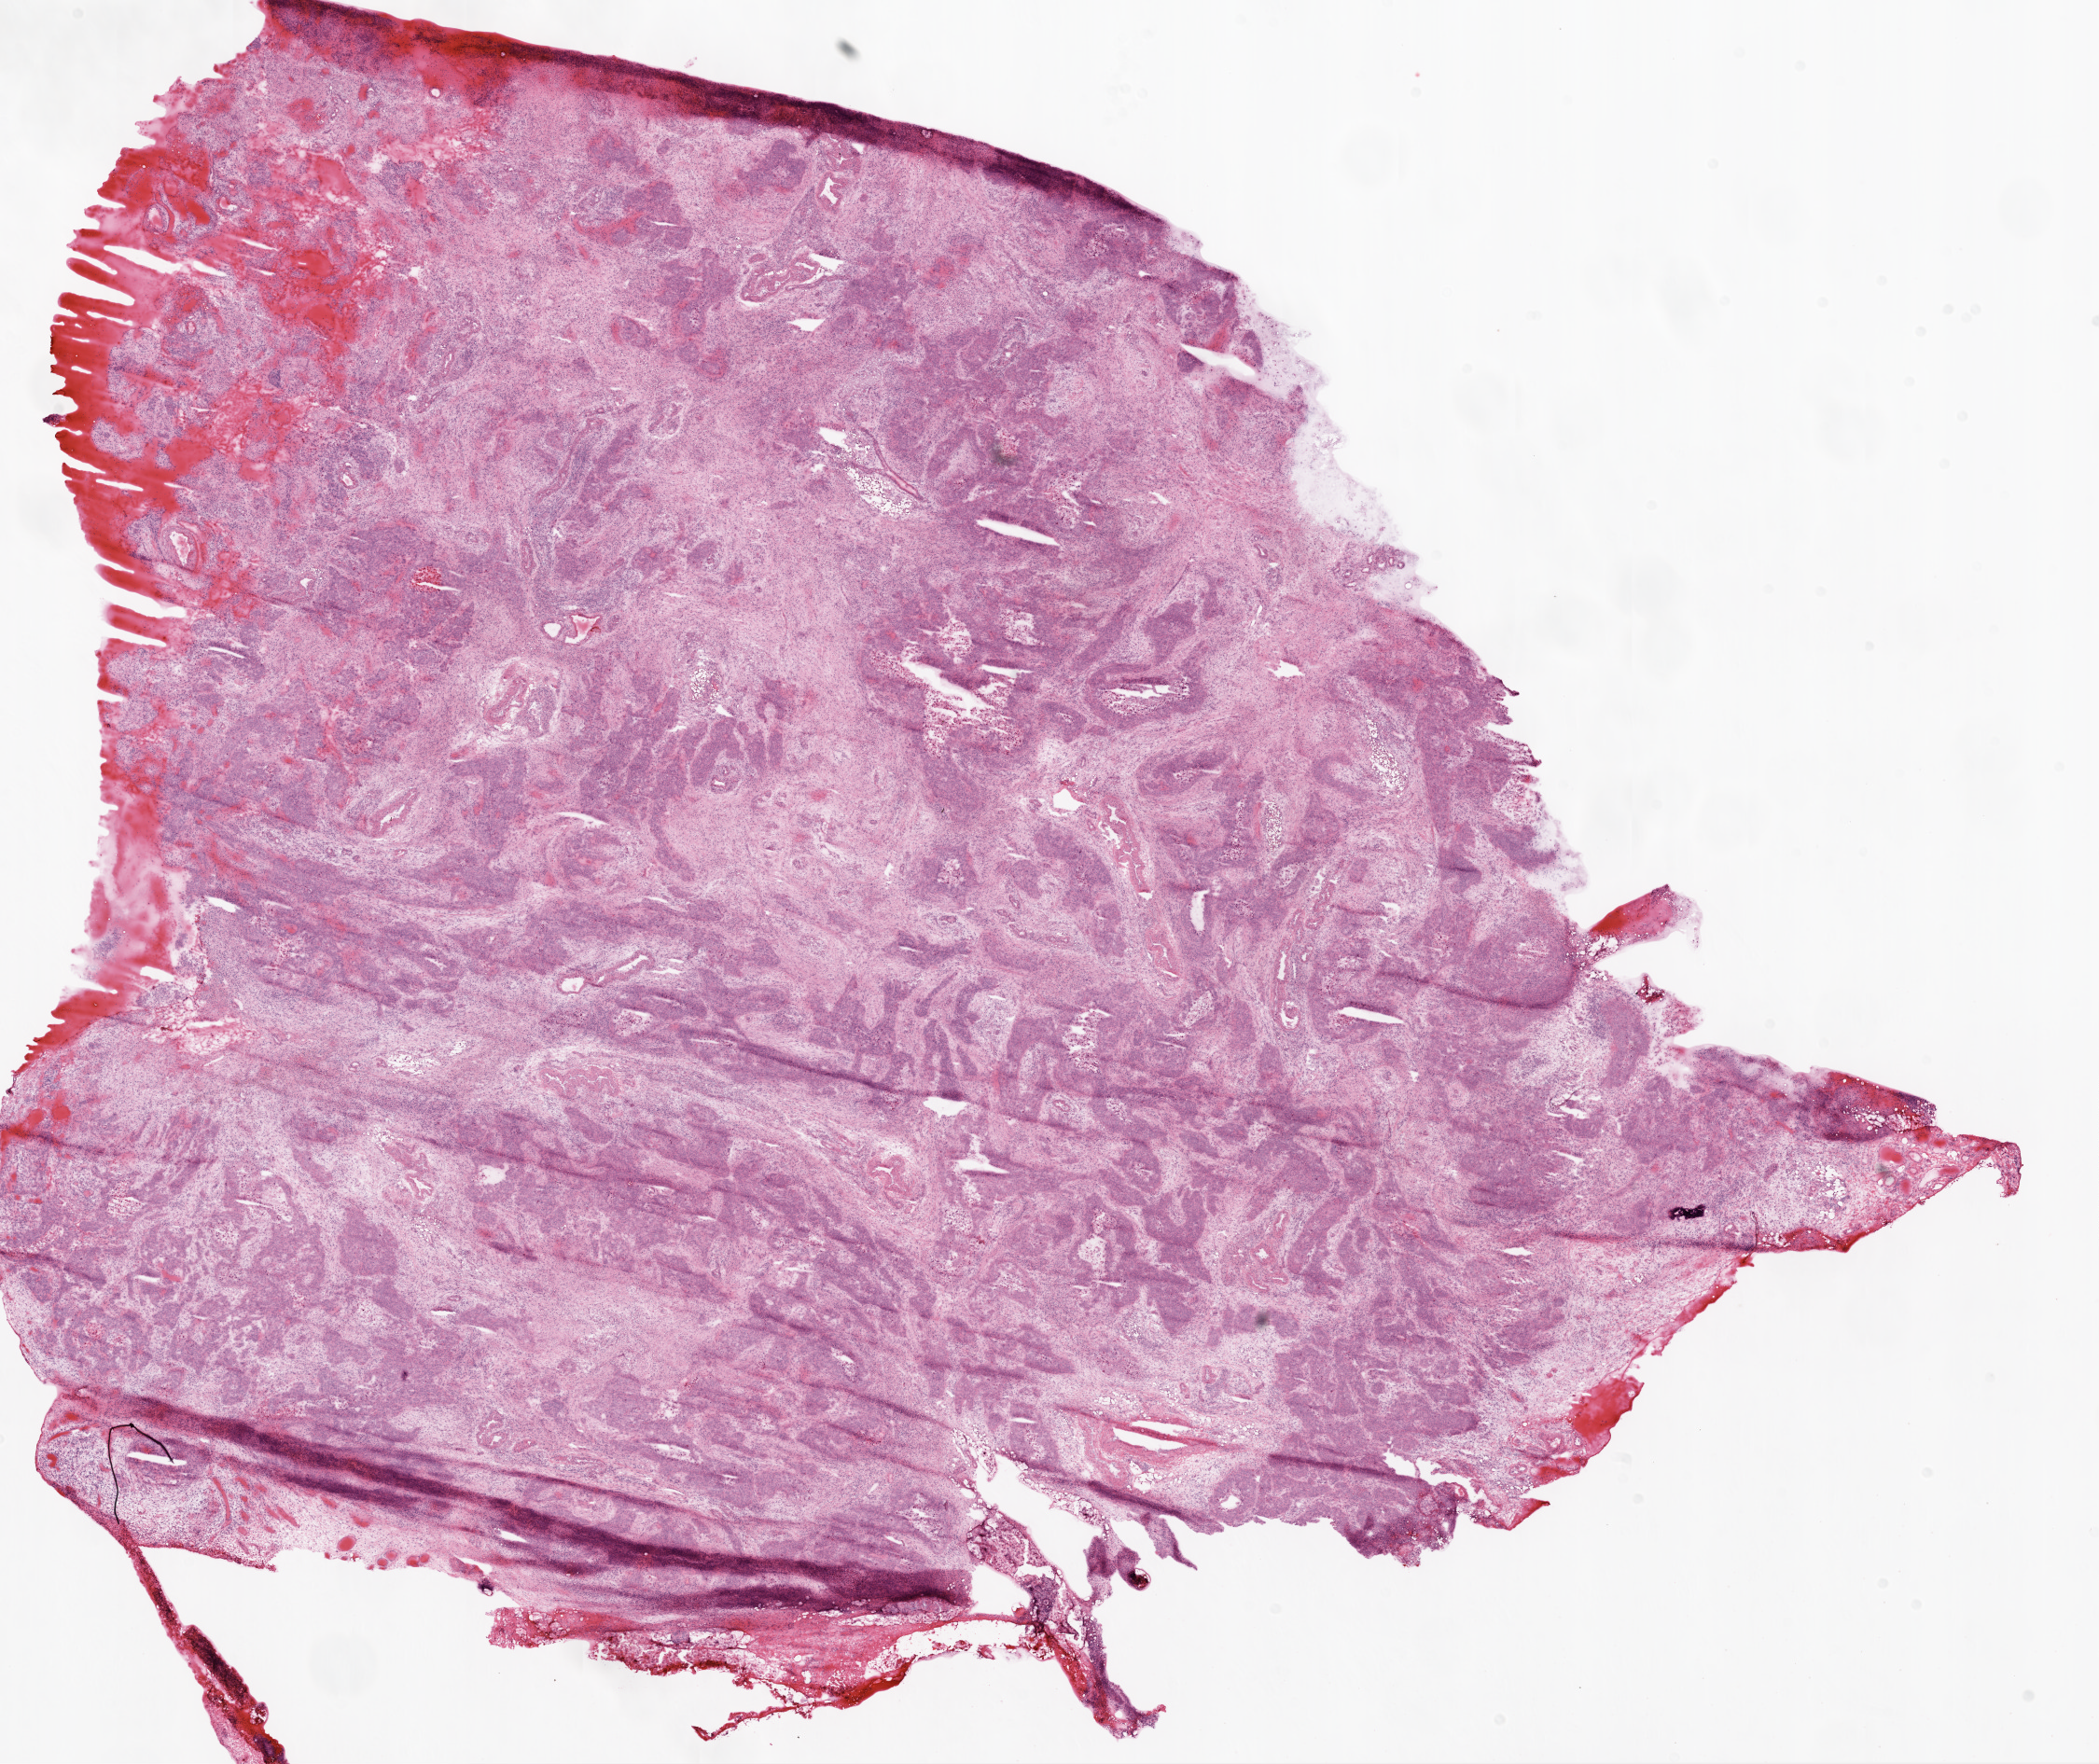
Whole-slide histology image, H&E-stained, shown as a low-resolution overview of the whole scanned area (about 18.1 x 15.2 mm, acquisition: 20x scan), frozen section from the top of the tissue portion, sample: primary tumour, ovary. Patient: female, age at initial diagnosis 71 years. Histologic grade: G3 (poorly differentiated). Slide review estimates, as recorded: tumour cells 55%, tumour nuclei 70%, normal cells 0%, stromal cells 40%, necrosis 5%.
Histologic diagnosis: Serous cystadenocarcinoma, NOS. FIGO stage: IV. Laterality: bilateral.